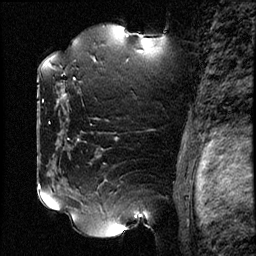
Breast MRI (dynamic contrast-enhanced), one sagittal slice. Slice 56 of 78 in the series (ordered by position). Dynamic contrast-enhanced study with each time point stored as its own series, time point 2 of 3 at this slice position (early post-contrast, ordered by acquisition time). 1.5 T. TE 4.2 ms, TR 17.6 ms. 2 mm slice thickness. 256 × 256 image matrix, field of view 200 × 200 mm. Female patient, age 42 years. Case-level facts recorded for this patient, not image findings: setting: breast cancer imaged before/during neoadjuvant chemotherapy; receptor status: HER2-positive.
Structures marked on this image (semi-automatic segmentation, software-assisted and operator-edited):
- analysis volume of interest (the breast-tissue region the enhancement analysis was run in; not a lesion): bounding box [x1, y1, x2, y2] px = [50, 48, 131, 129]
- tumour enhancement mask (voxels above the 100 % enhancement threshold inside the analysis volume of interest): [63, 94, 66, 97]